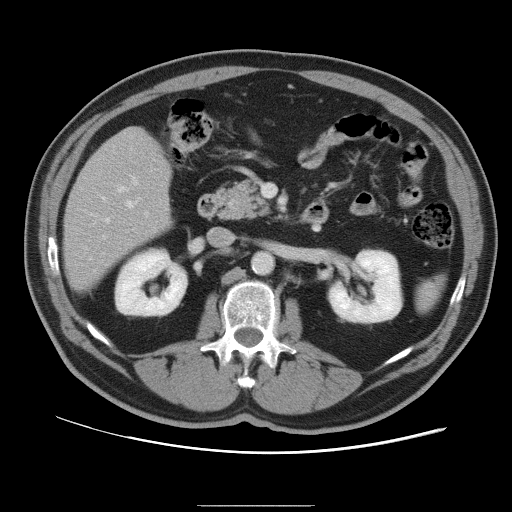
Contrast-enhanced abdominal CT, one axial slice. Slice 44 of 105 in the series (ordered by position). Intravenous contrast given. Soft-tissue window (W 400 / L 40 HU). 5 mm slice thickness. 512 × 512 image matrix, field of view 399 × 399 mm. Male patient, age 64 years. From the clinical record (not read from this slice): diagnosis: colorectal cancer liver metastases, imaged before liver resection; multiple liver metastases: yes; largest metastasis: 3 cm; disease in both lobes: yes.
Outlined on this slice (outlined manually by an expert reader):
- hepatic veins: bounding box (x1, y1, x2, y2) in pixels: (90, 201, 133, 259)
- liver: (65, 128, 171, 290)
- planned liver remnant (the part of the liver to remain after resection): (66, 129, 173, 291)
- portal vein (with intrahepatic branches): (103, 176, 138, 239)